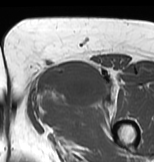
MRI of an extremity soft-tissue mass, one axial slice. Slice 40 of 83 in the series (ordered by position). MR volume resampled by the dataset authors to the PET/CT grid (not the native acquisition matrix). 154 × 162 image matrix, field of view 150 × 158 mm. Female patient. From the clinical record (not read from this slice): histological type: myxofibrosarcoma; grade: intermediate; site of the primary tumour: left thigh.
Annotated regions visible in this slice (expert contour drawn on MRI and transferred to this co-registered scan by the dataset authors):
- gross tumour volume including surrounding oedema: bounding box <26,63,120,119> (left, top, right, bottom; pixels)
- gross tumour volume (mass): <37,63,104,106>